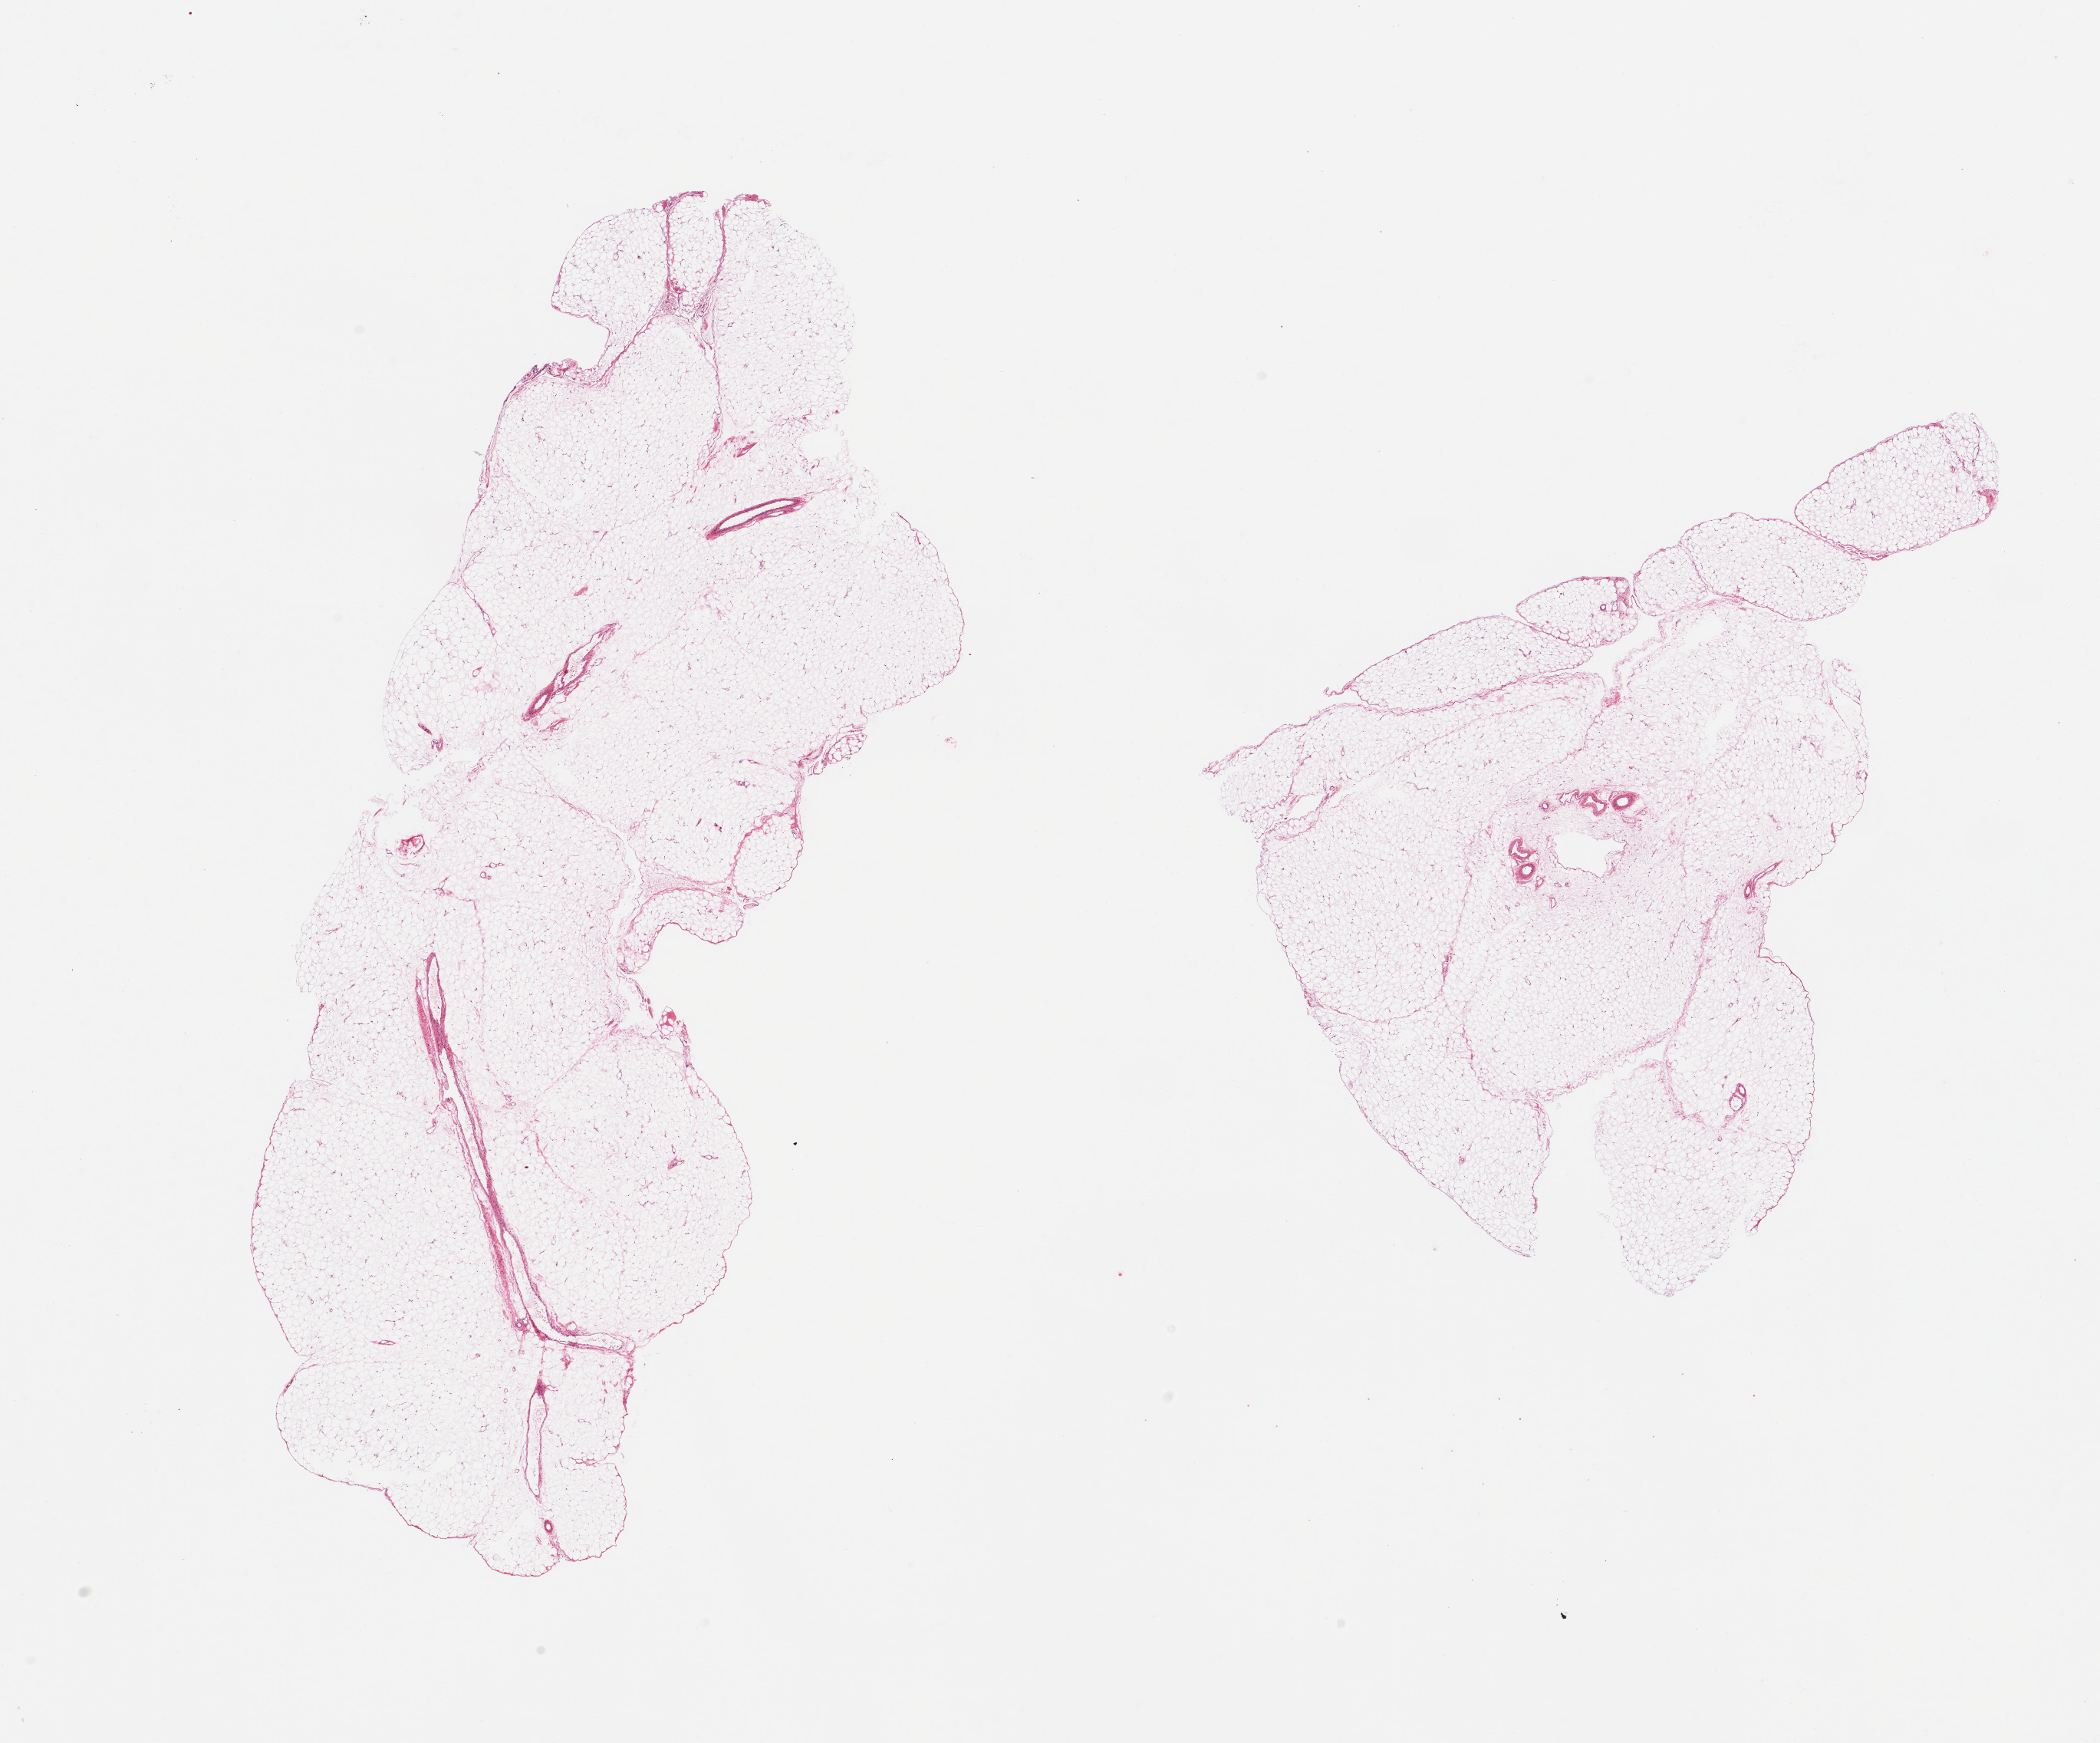
Whole-slide image, hematoxylin and eosin (H&E) stain, whole scanned area (about 21.7 x 18.0 mm, acquisition: 20x scan) shown as a low-resolution overview. PAXgene-fixed paraffin-embedded (PFPE) section. Sampled site (target tissue): omentum. Donor tissue sample.
Review note (as recorded): 2 pieces, ~5% vascular elements.